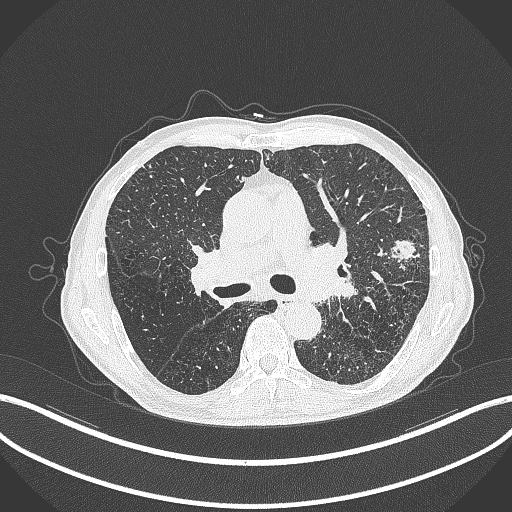
Chest CT, one axial slice. 120 kVp. Lung window (W 1500 / L -600 HU). 512 × 512 image matrix, field of view 400 × 400 mm. Patient: male, 74 years. Case-level facts recorded for this patient, not image findings: clinical TNM (as recorded): T2a N1 M0.
Structures marked on this image (rectangle marked by the reading radiologist):
- lung tumour (recorded histology: adenocarcinoma): bounding box <381,235,423,270> (left, top, right, bottom; pixels)